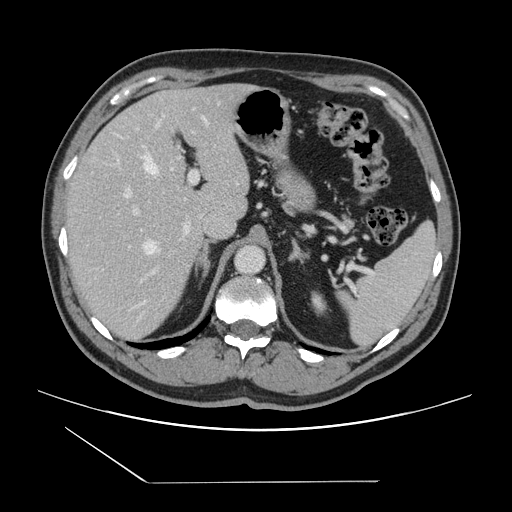
Contrast-enhanced abdominal CT, one axial slice; slice 97 of 157 in the series (ordered by position); intravenous contrast given; soft-tissue window (W 400 / L 40 HU); 2.5 mm slice thickness; 512 × 512 image matrix, field of view 407 × 407 mm. Male patient, age 61 years. Case-level facts recorded for this patient, not image findings: diagnosis: colorectal cancer liver metastases, imaged before liver resection; multiple liver metastases: yes; largest metastasis: 5.5 cm; disease in both lobes: yes.
Annotated regions visible in this slice (expert manual segmentation):
- hepatic veins: bounding box <144,117,206,254> (left, top, right, bottom; pixels)
- liver: <65,85,250,341>
- planned liver remnant (the part of the liver to remain after resection): <68,85,238,223>
- portal vein (with intrahepatic branches): <117,160,201,273>